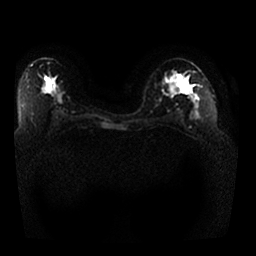
Breast MRI, one axial slice. Slice 15 of 25 in the series (ordered by position). Diffusion-weighted series; image 2 of 4 stored at this slice position (different b-values; order by instance number). 1.5 T. 4 mm slice thickness. 256 × 256 image matrix, field of view 350 × 350 mm. Female patient.
Outlined on this slice (outlined manually by an expert reader):
- tumour on diffusion-weighted imaging: bounding box [x1, y1, x2, y2] px = [180, 85, 186, 92]